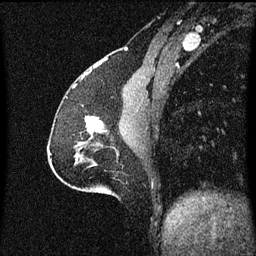
Breast MRI (dynamic contrast-enhanced), one sagittal slice. Slice 24 of 60 in the series (ordered by position). Dynamic contrast-enhanced series, image 2 of 3 at this slice position (ordered by acquisition). 1.5 T. TE 4.2 ms, TR 8.4 ms. 2 mm slice thickness. 256 × 256 image matrix, field of view 200 × 200 mm. Patient: female, 51 years.
Structures marked on this image (semi-automatically segmented with operator editing):
- analysis volume of interest (the breast-tissue region the enhancement analysis was run in; not a lesion): bounding box [x1, y1, x2, y2] px = [85, 116, 109, 139]
- tumour enhancement mask (voxels above the 70 % enhancement threshold inside the analysis volume of interest): [85, 116, 103, 133]